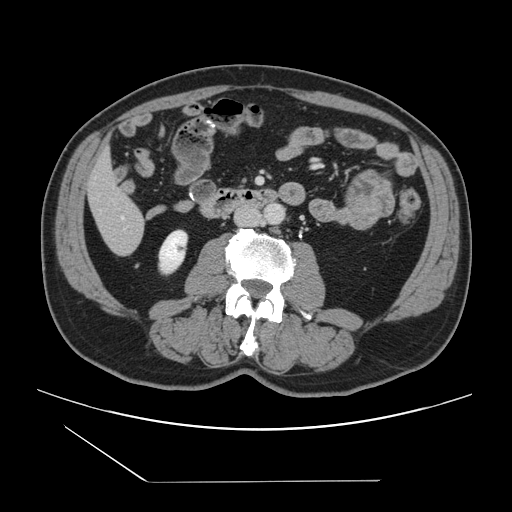
Contrast-enhanced abdominal CT, one axial slice; slice 27 of 157 in the series (ordered by position); 120 kVp; soft-tissue window (W 400 / L 40 HU); 2.5 mm slice thickness; 512 × 512 image matrix, field of view 407 × 407 mm. Male patient, age 61 years. From the clinical record (not read from this slice): diagnosis: colorectal cancer liver metastases, imaged before liver resection; multiple liver metastases: yes; largest metastasis: 5.5 cm; disease in both lobes: yes.
Structures marked on this image (manually delineated by an expert):
- liver: bounding box (x1, y1, x2, y2) in pixels: (89, 155, 145, 255)
- planned liver remnant (the part of the liver to remain after resection): (89, 154, 138, 218)